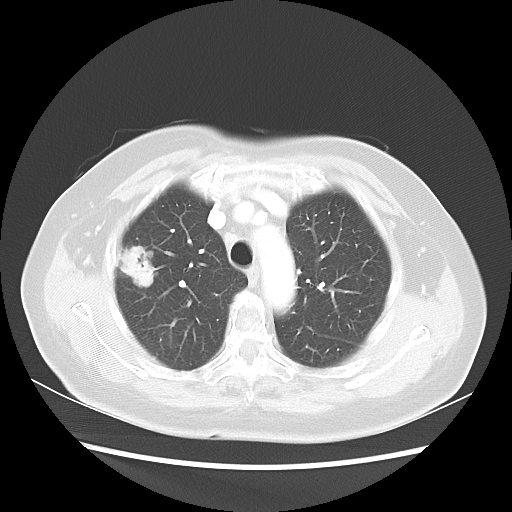
Chest CT, one axial slice. Position 36 of 48 along the scan axis. Reconstruction kernel LUNG. 100 kVp. Lung window (W 1500 / L -600 HU). 5 mm slice thickness. 512 × 512 image matrix, field of view 360 × 360 mm. Patient: female, 75 years. From the clinical record (not read from this slice): clinical TNM (as recorded): T1c N0 M0.
Structures marked on this image (rectangle marked by the reading radiologist):
- lung tumour (recorded histology: adenocarcinoma): bounding box (x1, y1, x2, y2) in pixels: (116, 242, 160, 296)